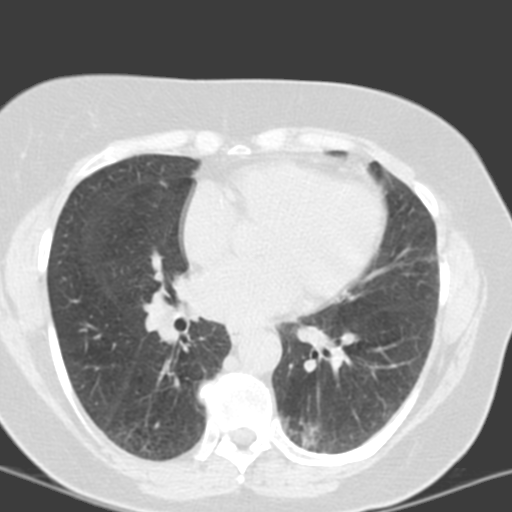
Chest CT (low-dose screening protocol), one axial image. Third annual screen. Lung window (W 1500 / L -600 HU). Standard (soft-tissue) reconstruction kernel (B). Slice 74 of 150 in the series. Female, age 55 years at enrolment. Current smoker at enrolment.
• Lesion marked by an expert reader, bounding box <275,403,357,461> (left, top, right, bottom; pixels).
• The screening reader recorded 6 non-calcified nodules or masses ≥4 mm on this exam (left lower lobe, left lower lobe, left upper lobe, lingula, lingula, right middle lobe); which of them this box marks is not recorded.
• Later outcome: lung cancer diagnosed 357 days after this screen — adenocarcinoma with mixed subtypes, left lower lobe, poorly differentiated (G3), stage IA (AJCC 6th edition), 21 mm at pathology.